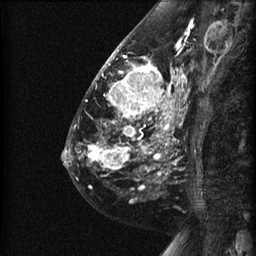
Breast MRI (dynamic contrast-enhanced), one sagittal slice. Position 24 of 60 along the scan axis. Dynamic contrast-enhanced series, image 2 of 3 at this slice position (ordered by acquisition). 1.5 T. TE 4.2 ms, TR 22.7 ms. 1.5 mm slice thickness. 256 × 256 image matrix. Patient: female, 48 years. Case-level facts recorded for this patient, not image findings: setting: breast cancer imaged before/during neoadjuvant chemotherapy; receptor status: triple-negative.
Annotated regions visible in this slice (semi-automatic segmentation, software-assisted and operator-edited):
- analysis volume of interest (the breast-tissue region the enhancement analysis was run in; not a lesion): bounding box [x1, y1, x2, y2] px = [89, 27, 191, 180]
- tumour enhancement mask (voxels above the 90 % enhancement threshold inside the analysis volume of interest): [89, 50, 182, 177]